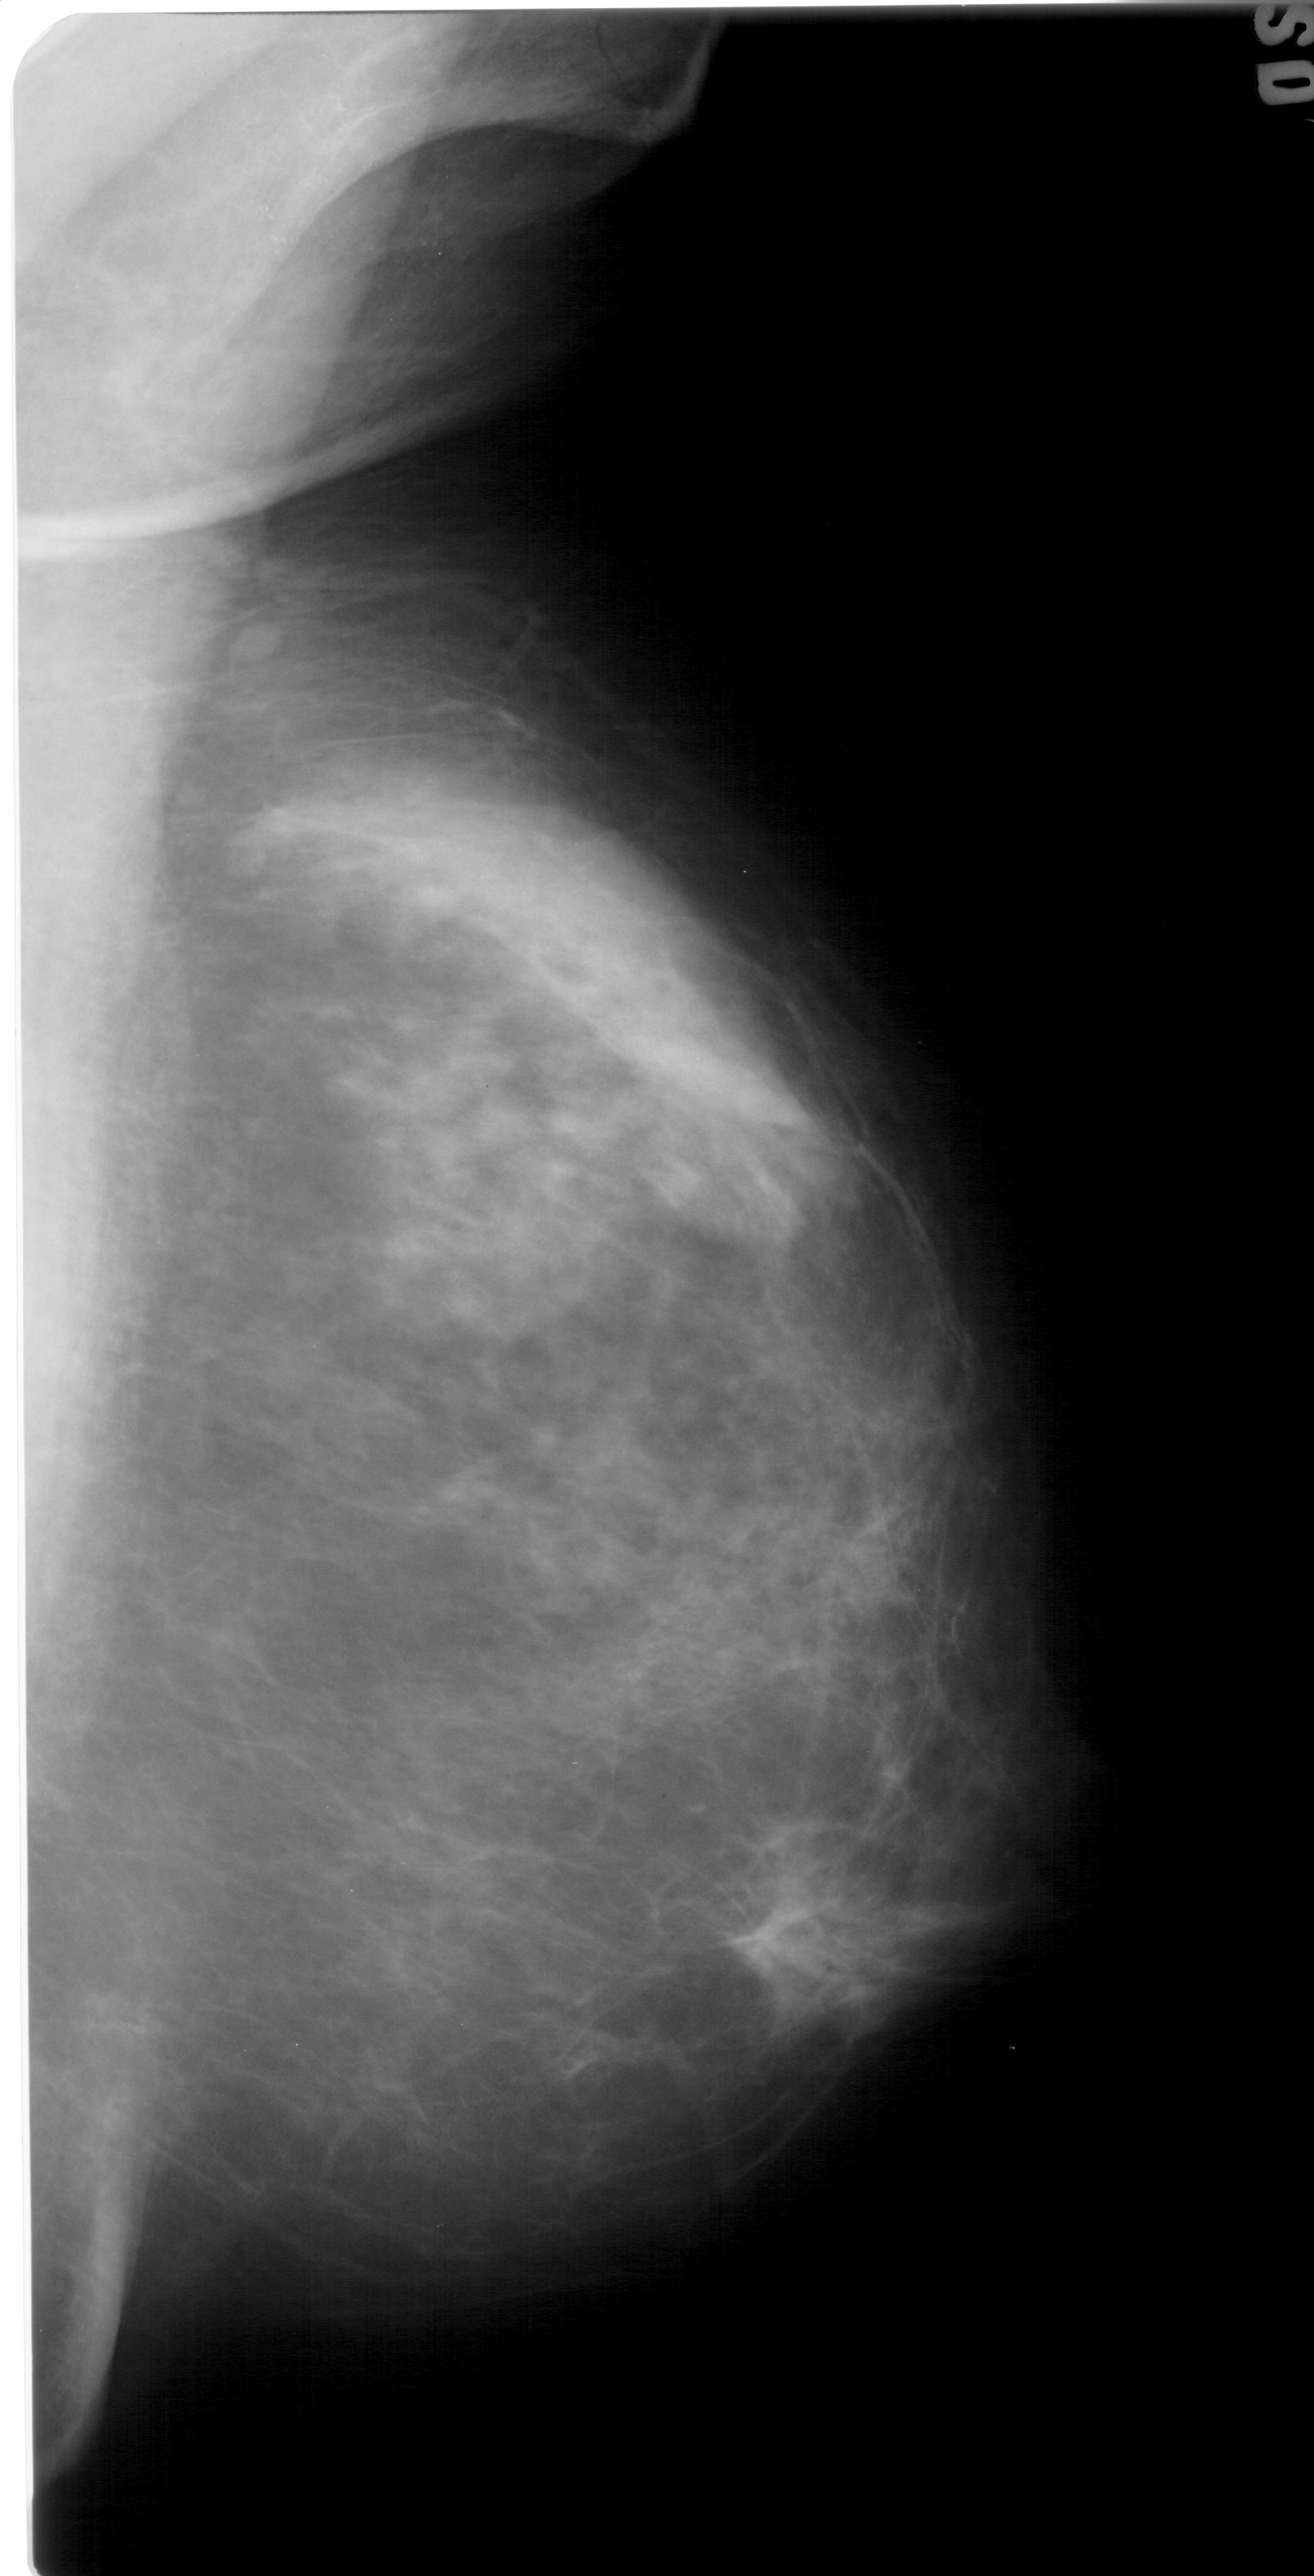
Mammogram (digitized film). Right breast. Mediolateral oblique (MLO) view. Breast composition: scattered fibroglandular densities (BI-RADS density category 2 of 4). 1314 × 2576 image matrix.
Marked abnormalities (boxes around the expert regions of interest):
- mass, shape asymmetric breast tissue, margins obscured; BI-RADS assessment category 4; outcome (as recorded, no biopsy): benign without callback (not worked up further): bounding box (x1, y1, x2, y2) in pixels: (445, 784, 771, 1059)